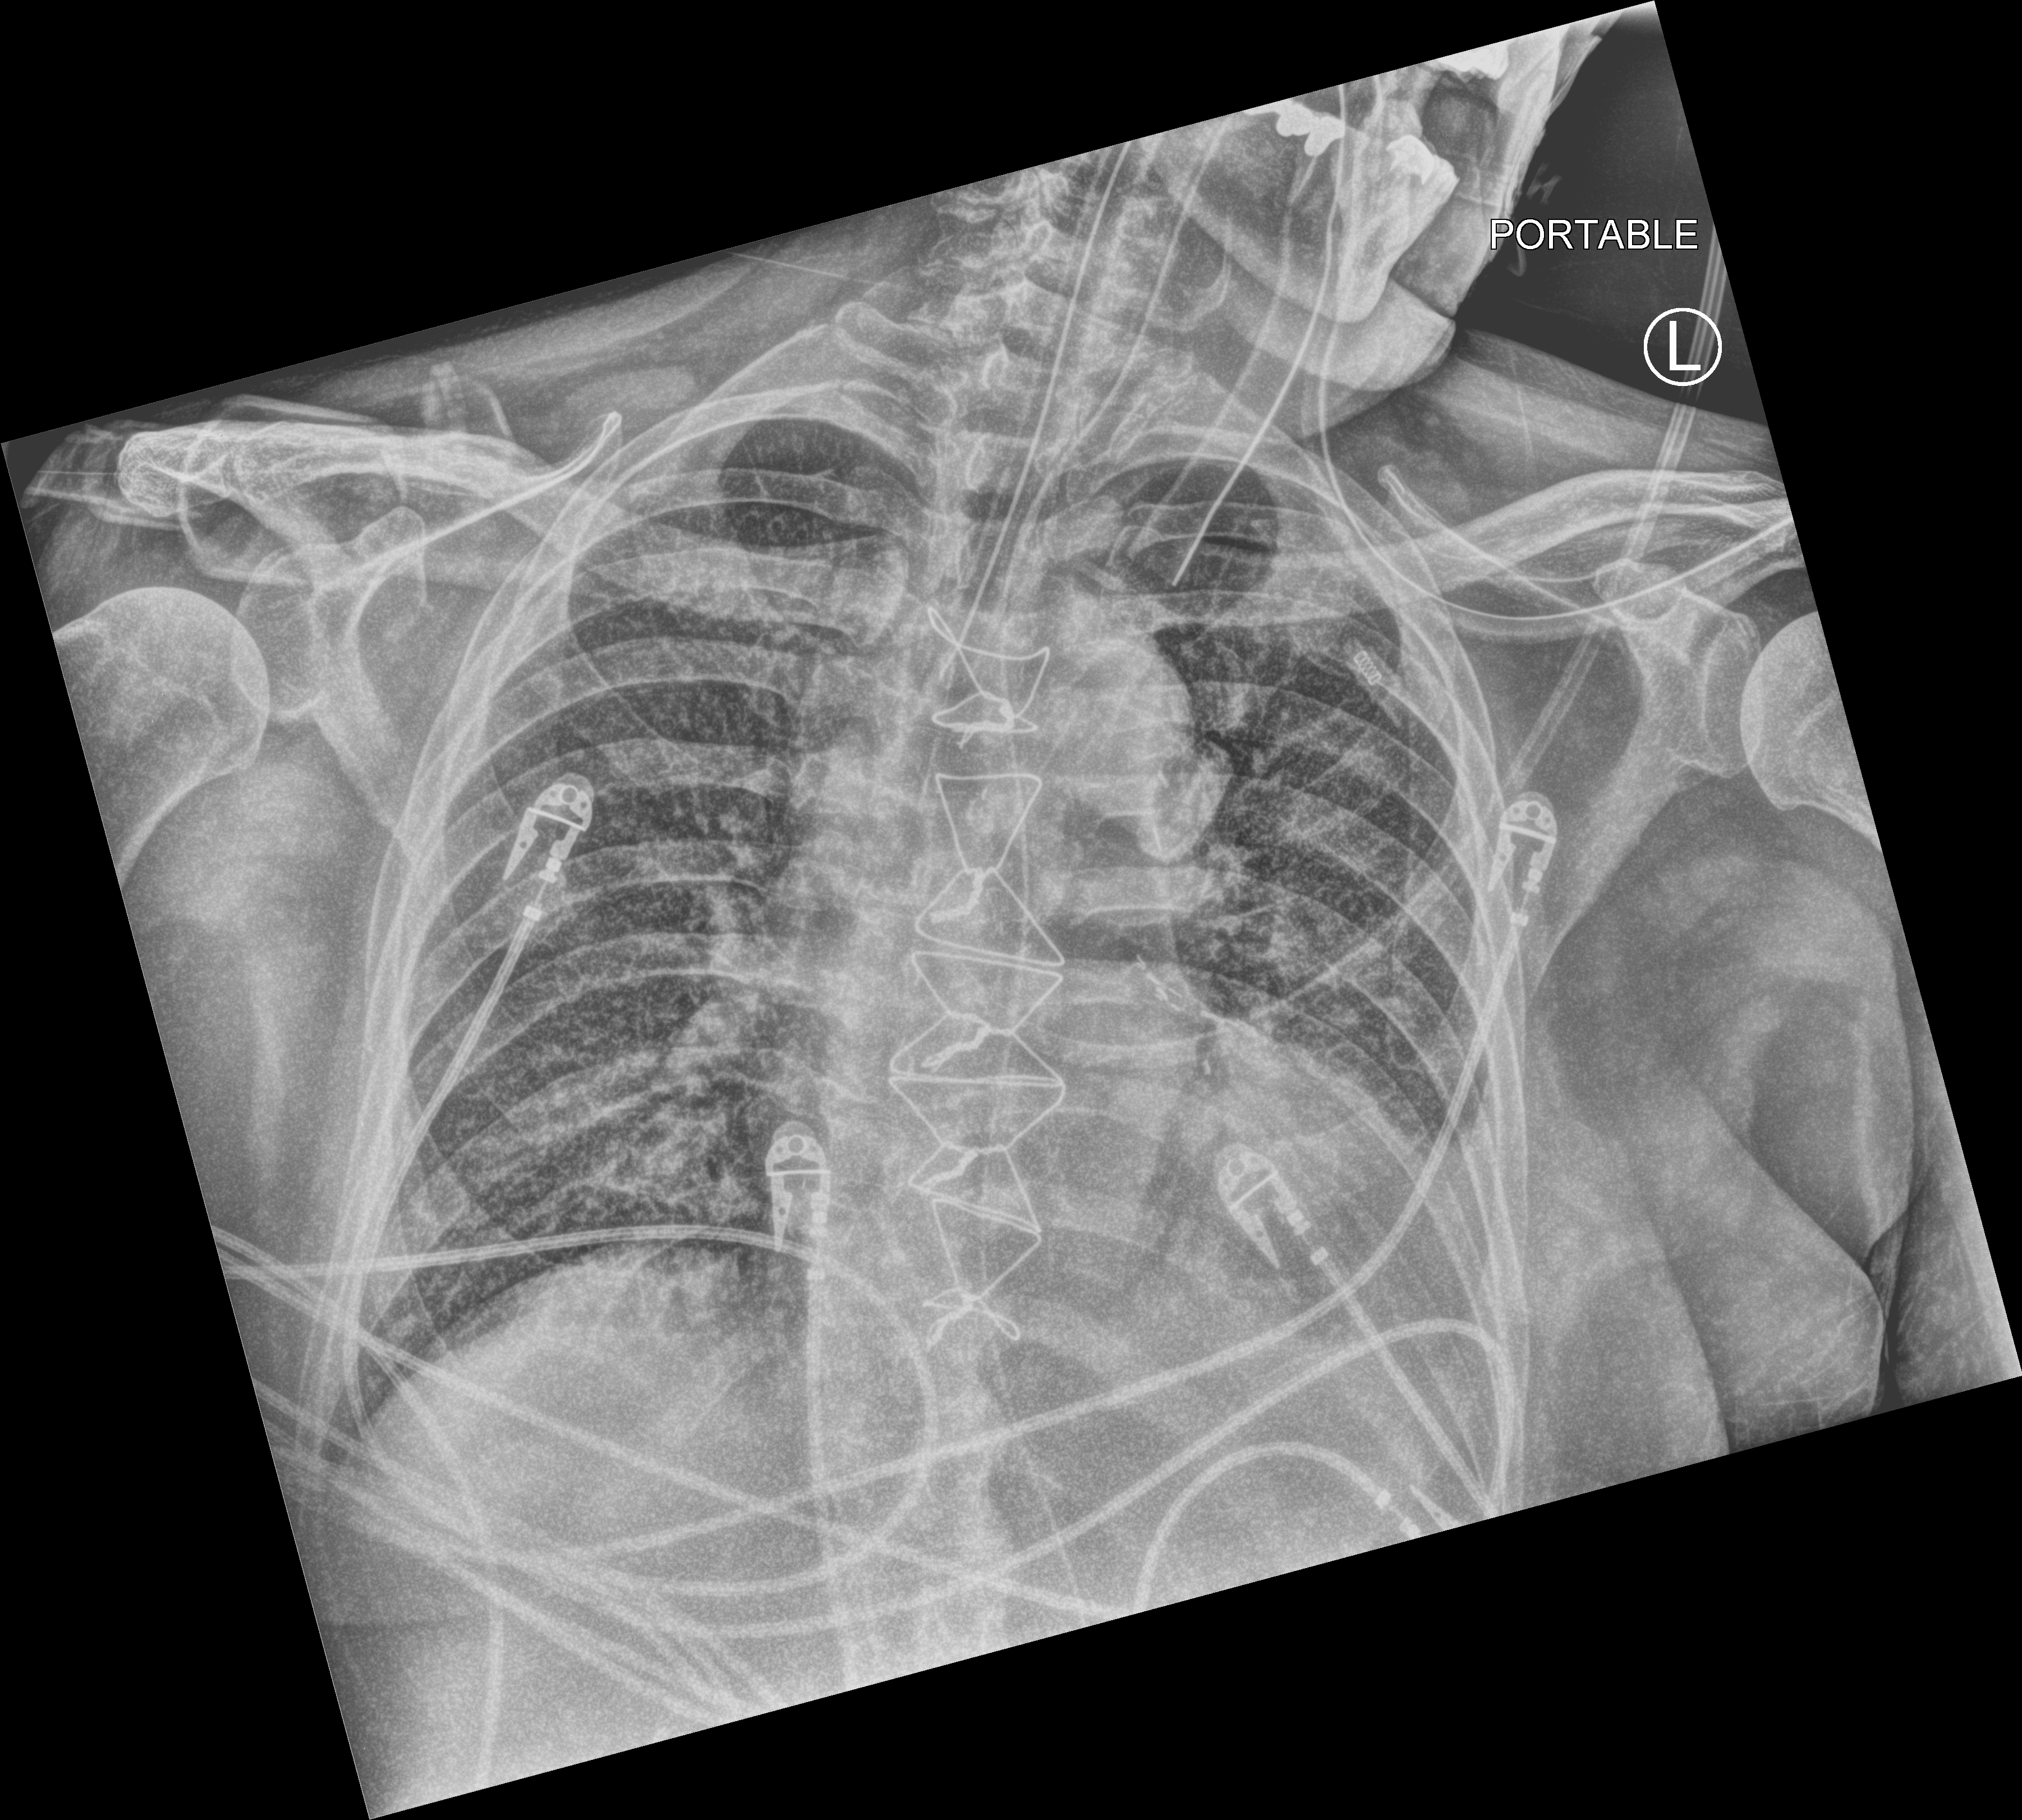
Chest X-ray (portable); anteroposterior (AP) projection. Male patient hospitalised with COVID-19, age 75–90 years.
Admission-level facts for this patient (not findings on this image; timing relative to this image not recorded):
- length of hospital stay: 28 days